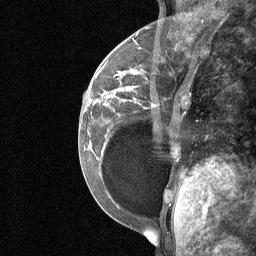
Breast MRI (dynamic contrast-enhanced), one sagittal slice; position 21 of 64 along the scan axis; dynamic contrast-enhanced study with each time point stored as its own series, time point 2 of 3 at this slice position (early post-contrast, ordered by acquisition time); 1.5 T; TE 4.8 ms, TR 27 ms; 256 × 256 image matrix, field of view 200 × 200 mm. Female patient, age 34 years. From the clinical record (not read from this slice): setting: breast cancer imaged before/during neoadjuvant chemotherapy; receptor status: HR-positive, HER2-negative.
Annotated regions visible in this slice (semi-automatically segmented with operator editing):
- analysis volume of interest (the breast-tissue region the enhancement analysis was run in; not a lesion): bounding box (x1, y1, x2, y2) in pixels: (92, 50, 188, 185)
- tumour enhancement mask (voxels above the 90 % enhancement threshold inside the analysis volume of interest): (119, 72, 137, 89)